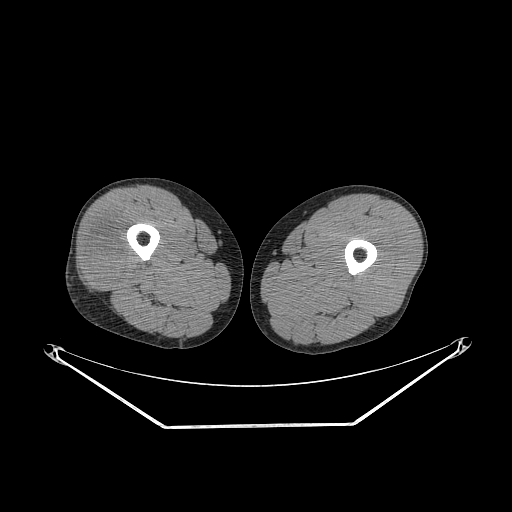
CT of an extremity soft-tissue mass (from a PET/CT study), one axial slice. Position 234 of 267 along the scan axis. Reconstruction kernel STANDARD. 140 kVp. Soft-tissue window (W 400 / L 40 HU). 3.75 mm slice thickness. 512 × 512 image matrix. Male patient. Case-level facts recorded for this patient, not image findings: histological type: poorly differentiated synovial sarcoma; grade: high; site of the primary tumour: right buttock.
Outlined on this slice (expert contour drawn on MRI and transferred to this co-registered scan by the dataset authors):
- gross tumour volume including surrounding oedema: bounding box <87,219,131,286> (left, top, right, bottom; pixels)
- gross tumour volume (mass): <89,230,131,286>